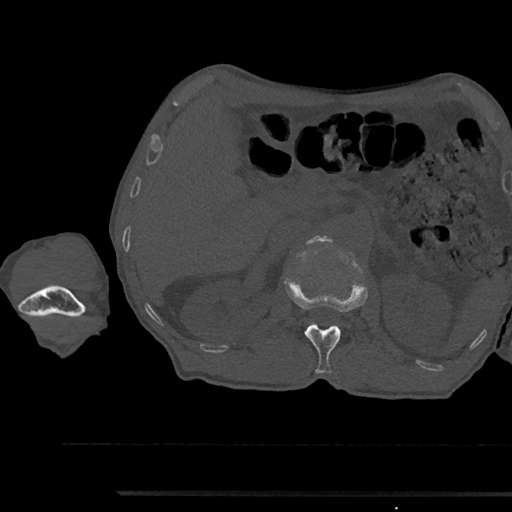
CT including the spine, one axial slice; position 622 of 797 along the scan axis; bone window (W 1800 / L 400 HU); 0.5 mm slice thickness; 512 × 512 image matrix. Patient: male, 79 years. From the clinical record (not read from this slice): primary cancer: prostate.
Structures marked on this image (semi-automatic segmentation, software-assisted and operator-edited):
- L1 vertebra: bounding box <285,279,367,374> (left, top, right, bottom; pixels)
- L2 vertebra: <307,236,333,244>